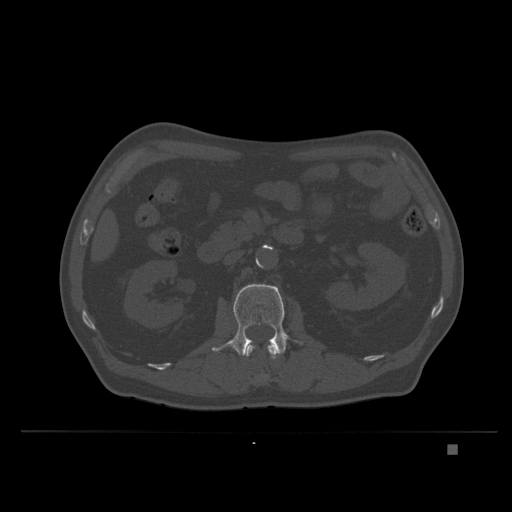
CT including the spine, one axial slice; slice 122 of 435 in the series (ordered by position); bone window (W 1800 / L 400 HU); 1.5 mm slice thickness; 512 × 512 image matrix, field of view 434 × 434 mm. Patient: male, 73 years. From the clinical record (not read from this slice): primary cancer: skin.
Structures marked on this image (semi-automatic segmentation, software-assisted and operator-edited):
- L1 vertebra: box from (x=246, y=342) to (x=277, y=381) px
- L2 vertebra: (x=212, y=284)–(x=302, y=358)